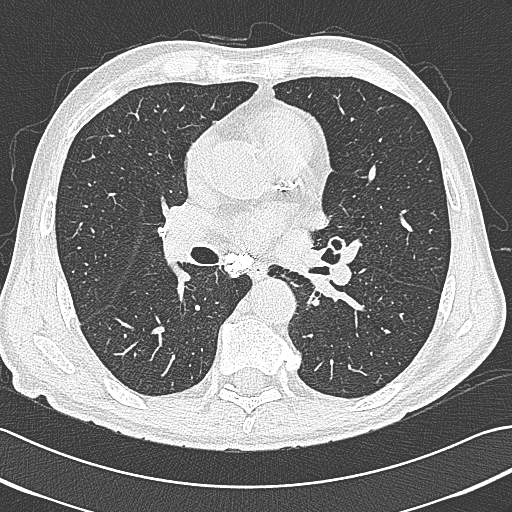
Axial slice from a low-dose chest CT screening exam, baseline screening round, lung window (W 1500 / L -600 HU), 1 mm slice thickness, slice 183 of 380 in the series, 512 × 512 image matrix. Male, age 65 years at enrolment.
Expert-annotated lung lesion, bounding box (x1, y1, x2, y2) in pixels: (305, 233, 355, 273). Screening reader's record for this exam: no non-calcified nodule ≥4 mm recorded. Lung cancer was diagnosed 161 days after this screen: large cell neuroendocrine carcinoma, left hilum, left main stem bronchus, stage IIIB (AJCC 6th edition), 70 mm at pathology.